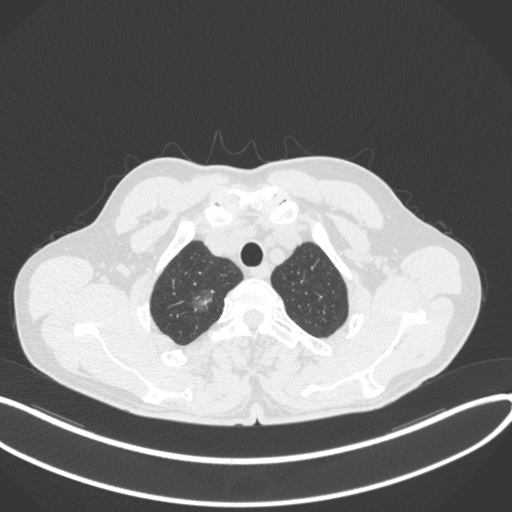
Chest CT, one axial slice. Slice 338 of 407 in the series (ordered by position). Reconstruction kernel B31f. Lung window (W 1500 / L -600 HU). 1 mm slice thickness. 512 × 512 image matrix. Patient: male, 58 years. Case-level facts recorded for this patient, not image findings: clinical TNM (as recorded): T1c N0 M0; histopathological grade: G1-2.
Structures marked on this image (bounding box drawn by a radiologist):
- lung tumour (recorded histology: adenocarcinoma): bounding box [x1, y1, x2, y2] px = [188, 283, 220, 316]